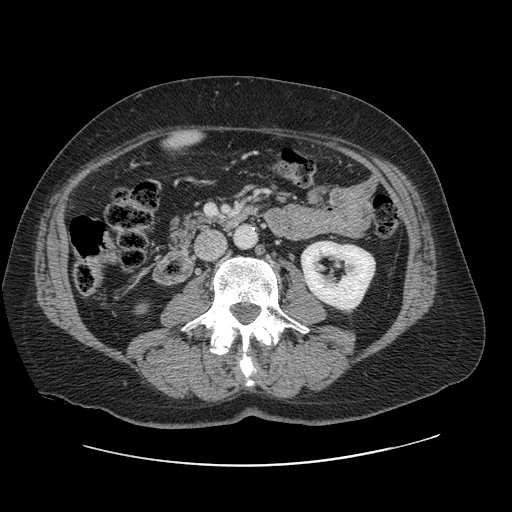
Contrast-enhanced abdominal CT, one axial slice. Position 13 of 138 along the scan axis. Soft-tissue window (W 400 / L 40 HU). 512 × 512 image matrix, field of view 402 × 402 mm. Male patient, age 71 years. From the clinical record (not read from this slice): diagnosis: colorectal cancer liver metastases, imaged before liver resection; multiple liver metastases: no; largest metastasis: 3.3 cm; disease in both lobes: no.
Structures marked on this image (expert manual segmentation):
- liver: box from (x=169, y=133) to (x=197, y=147) px